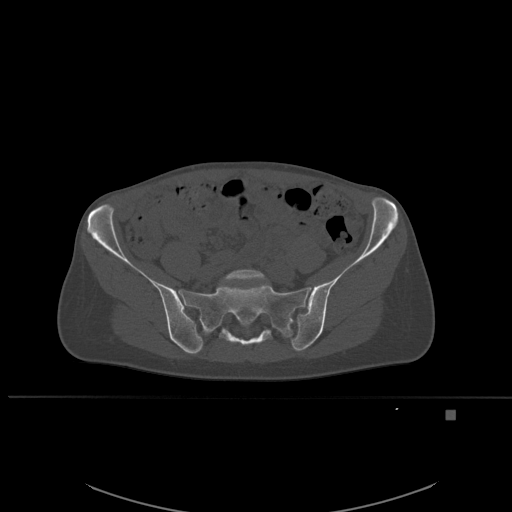
CT including the spine, one axial slice; position 156 of 537 along the scan axis; bone window (W 1800 / L 400 HU); 1.5 mm slice thickness; 512 × 512 image matrix, field of view 440 × 440 mm. Female patient, age 45 years. Case-level facts recorded for this patient, not image findings: primary cancer: lung.
Structures marked on this image (semi-automatically segmented with operator editing):
- L5 vertebra: bounding box <219,269,266,285> (left, top, right, bottom; pixels)